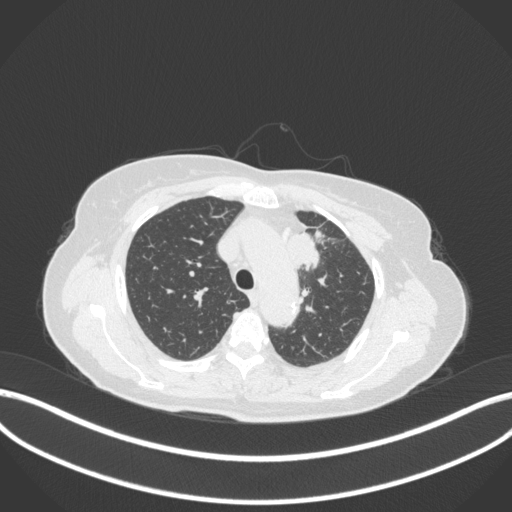
Chest CT, one axial slice. Position 250 of 368 along the scan axis. Lung window (W 1500 / L -600 HU). 1 mm slice thickness. 512 × 512 image matrix, field of view 400 × 400 mm. Female patient, age 65 years. From the clinical record (not read from this slice): clinical TNM (as recorded): T2a N0 M0; histopathological grade: G2-3.
Annotated regions visible in this slice (bounding box drawn by a radiologist):
- lung tumour (recorded histology: adenocarcinoma): bounding box <284,228,320,276> (left, top, right, bottom; pixels)